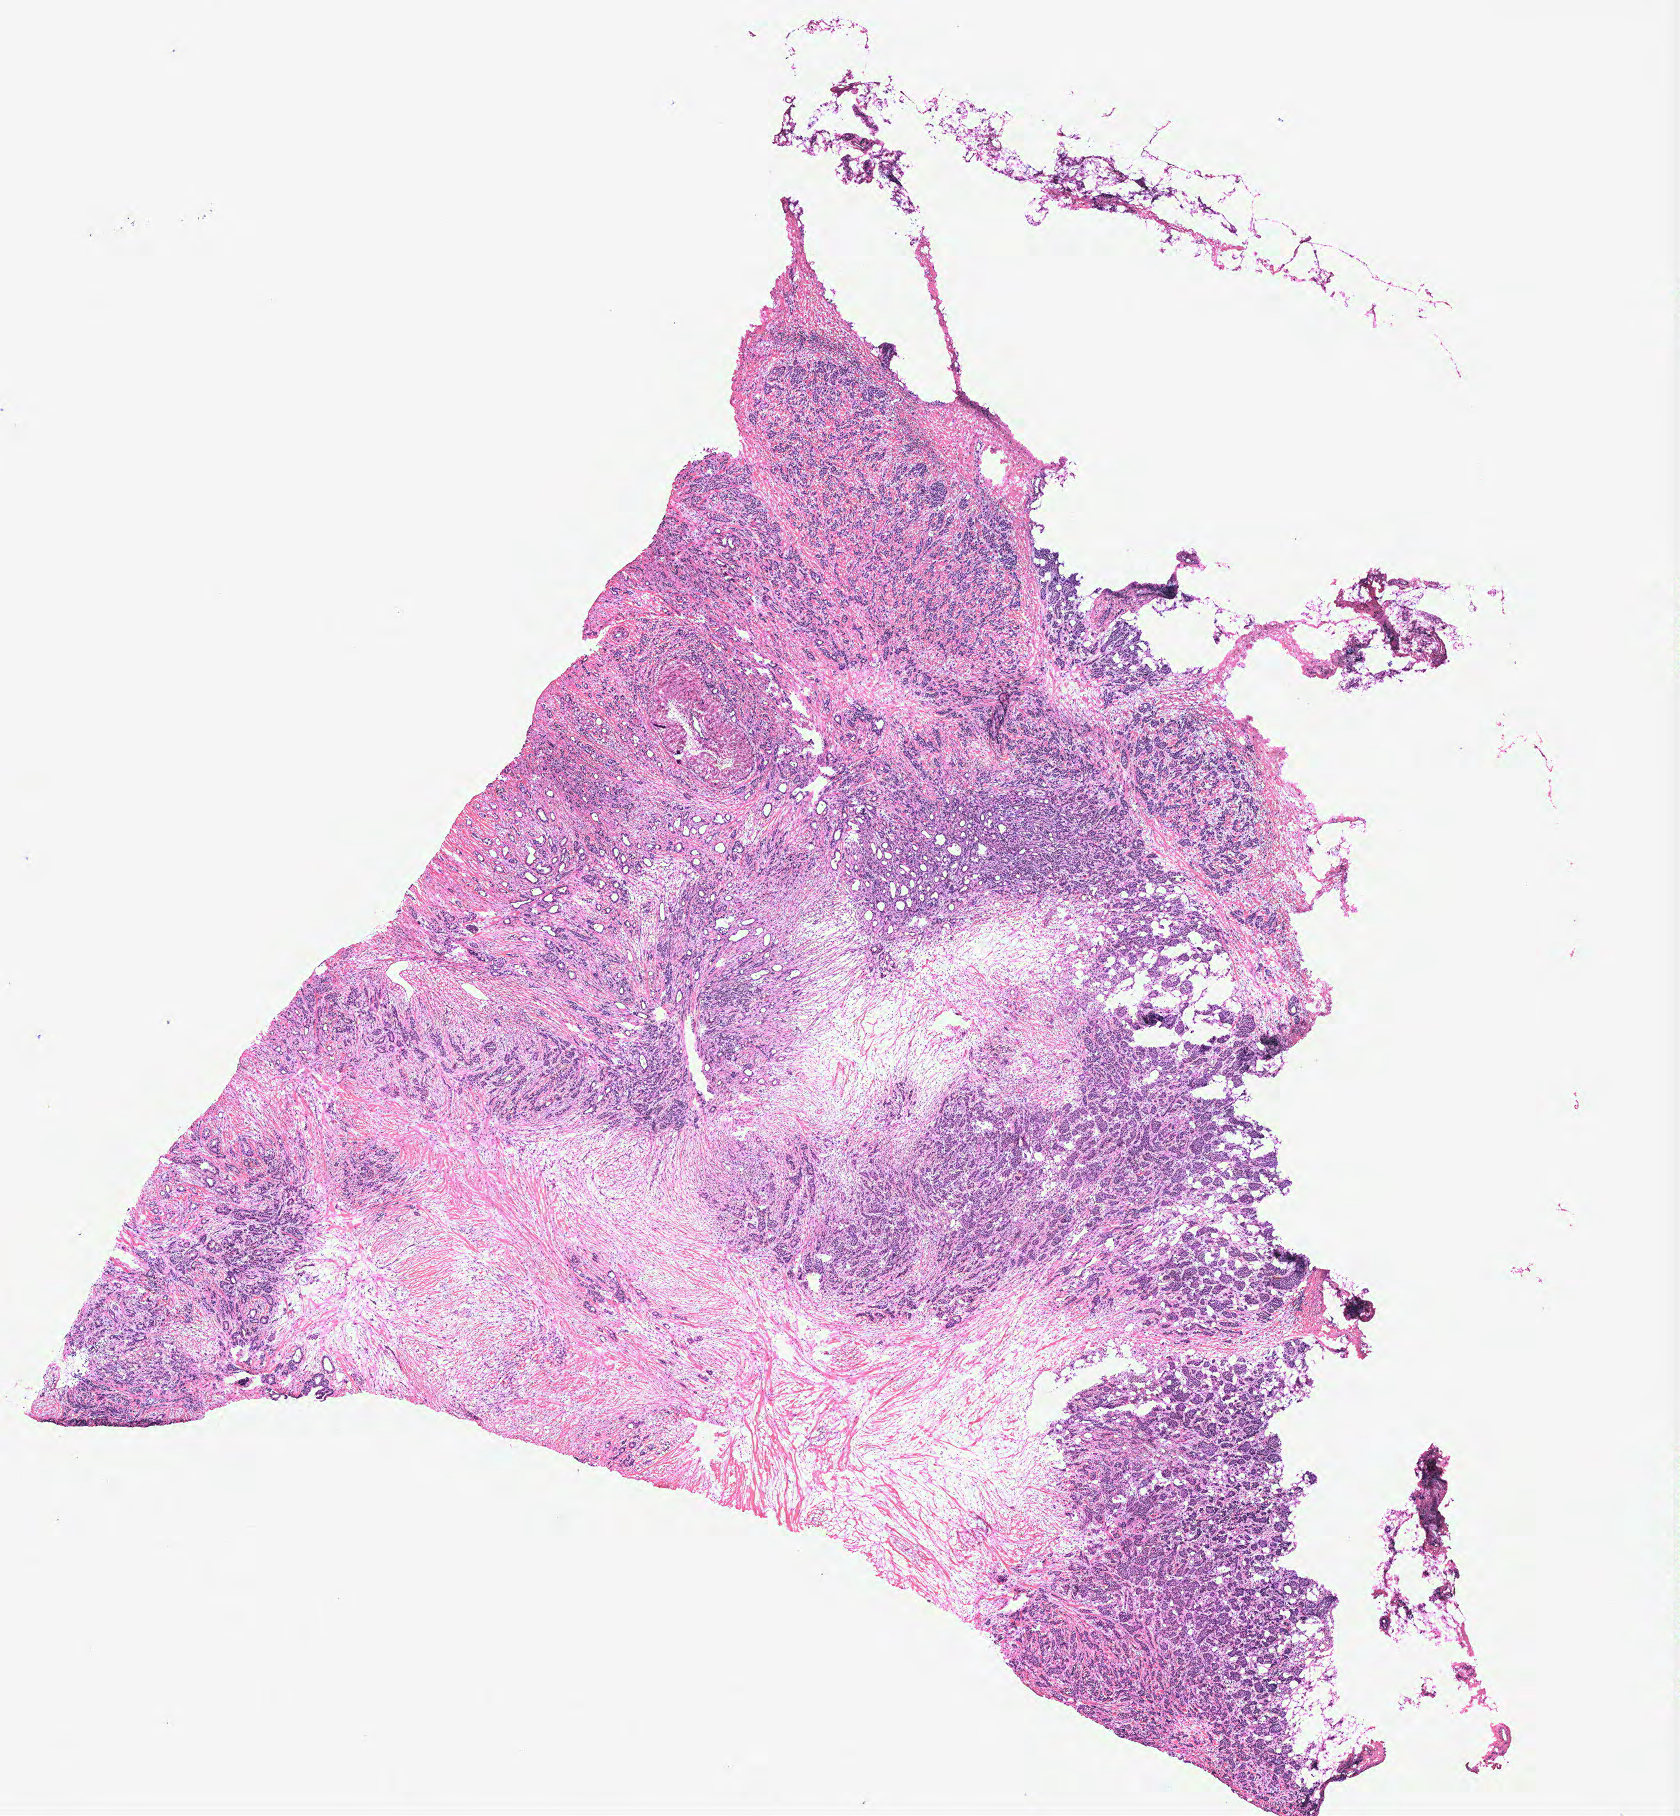
H&E whole-slide image, a low-resolution overview of the entire scanned area, about 13.4 x 14.5 mm (acquisition: 40x scan). Breast, tissue type not recorded. Patient: female, age 73 years.
Patient diagnosis: Infiltrating duct carcinoma, NOS.